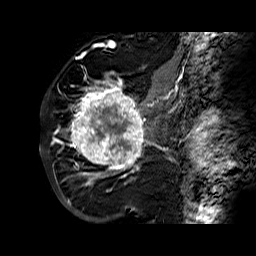
Breast MRI (dynamic contrast-enhanced), one sagittal slice. Slice 39 of 60 in the series (ordered by position). Dynamic contrast-enhanced series, time point 2 of 6 at this slice position (early post-contrast). 1.5 T. TE 6.3 ms, TR 32.4 ms. 4 mm slice thickness. 256 × 256 image matrix, field of view 200 × 200 mm. Female patient. Case-level facts recorded for this patient, not image findings: setting: breast cancer imaged before/during neoadjuvant chemotherapy; receptor status: HR-positive, HER2-negative.
Outlined on this slice (semi-automatic segmentation, software-assisted and operator-edited):
- analysis volume of interest (the breast-tissue region the enhancement analysis was run in; not a lesion): box from (x=68, y=72) to (x=177, y=183) px
- tumour enhancement mask (voxels above the 100 % enhancement threshold inside the analysis volume of interest): (x=70, y=72)–(x=172, y=183)